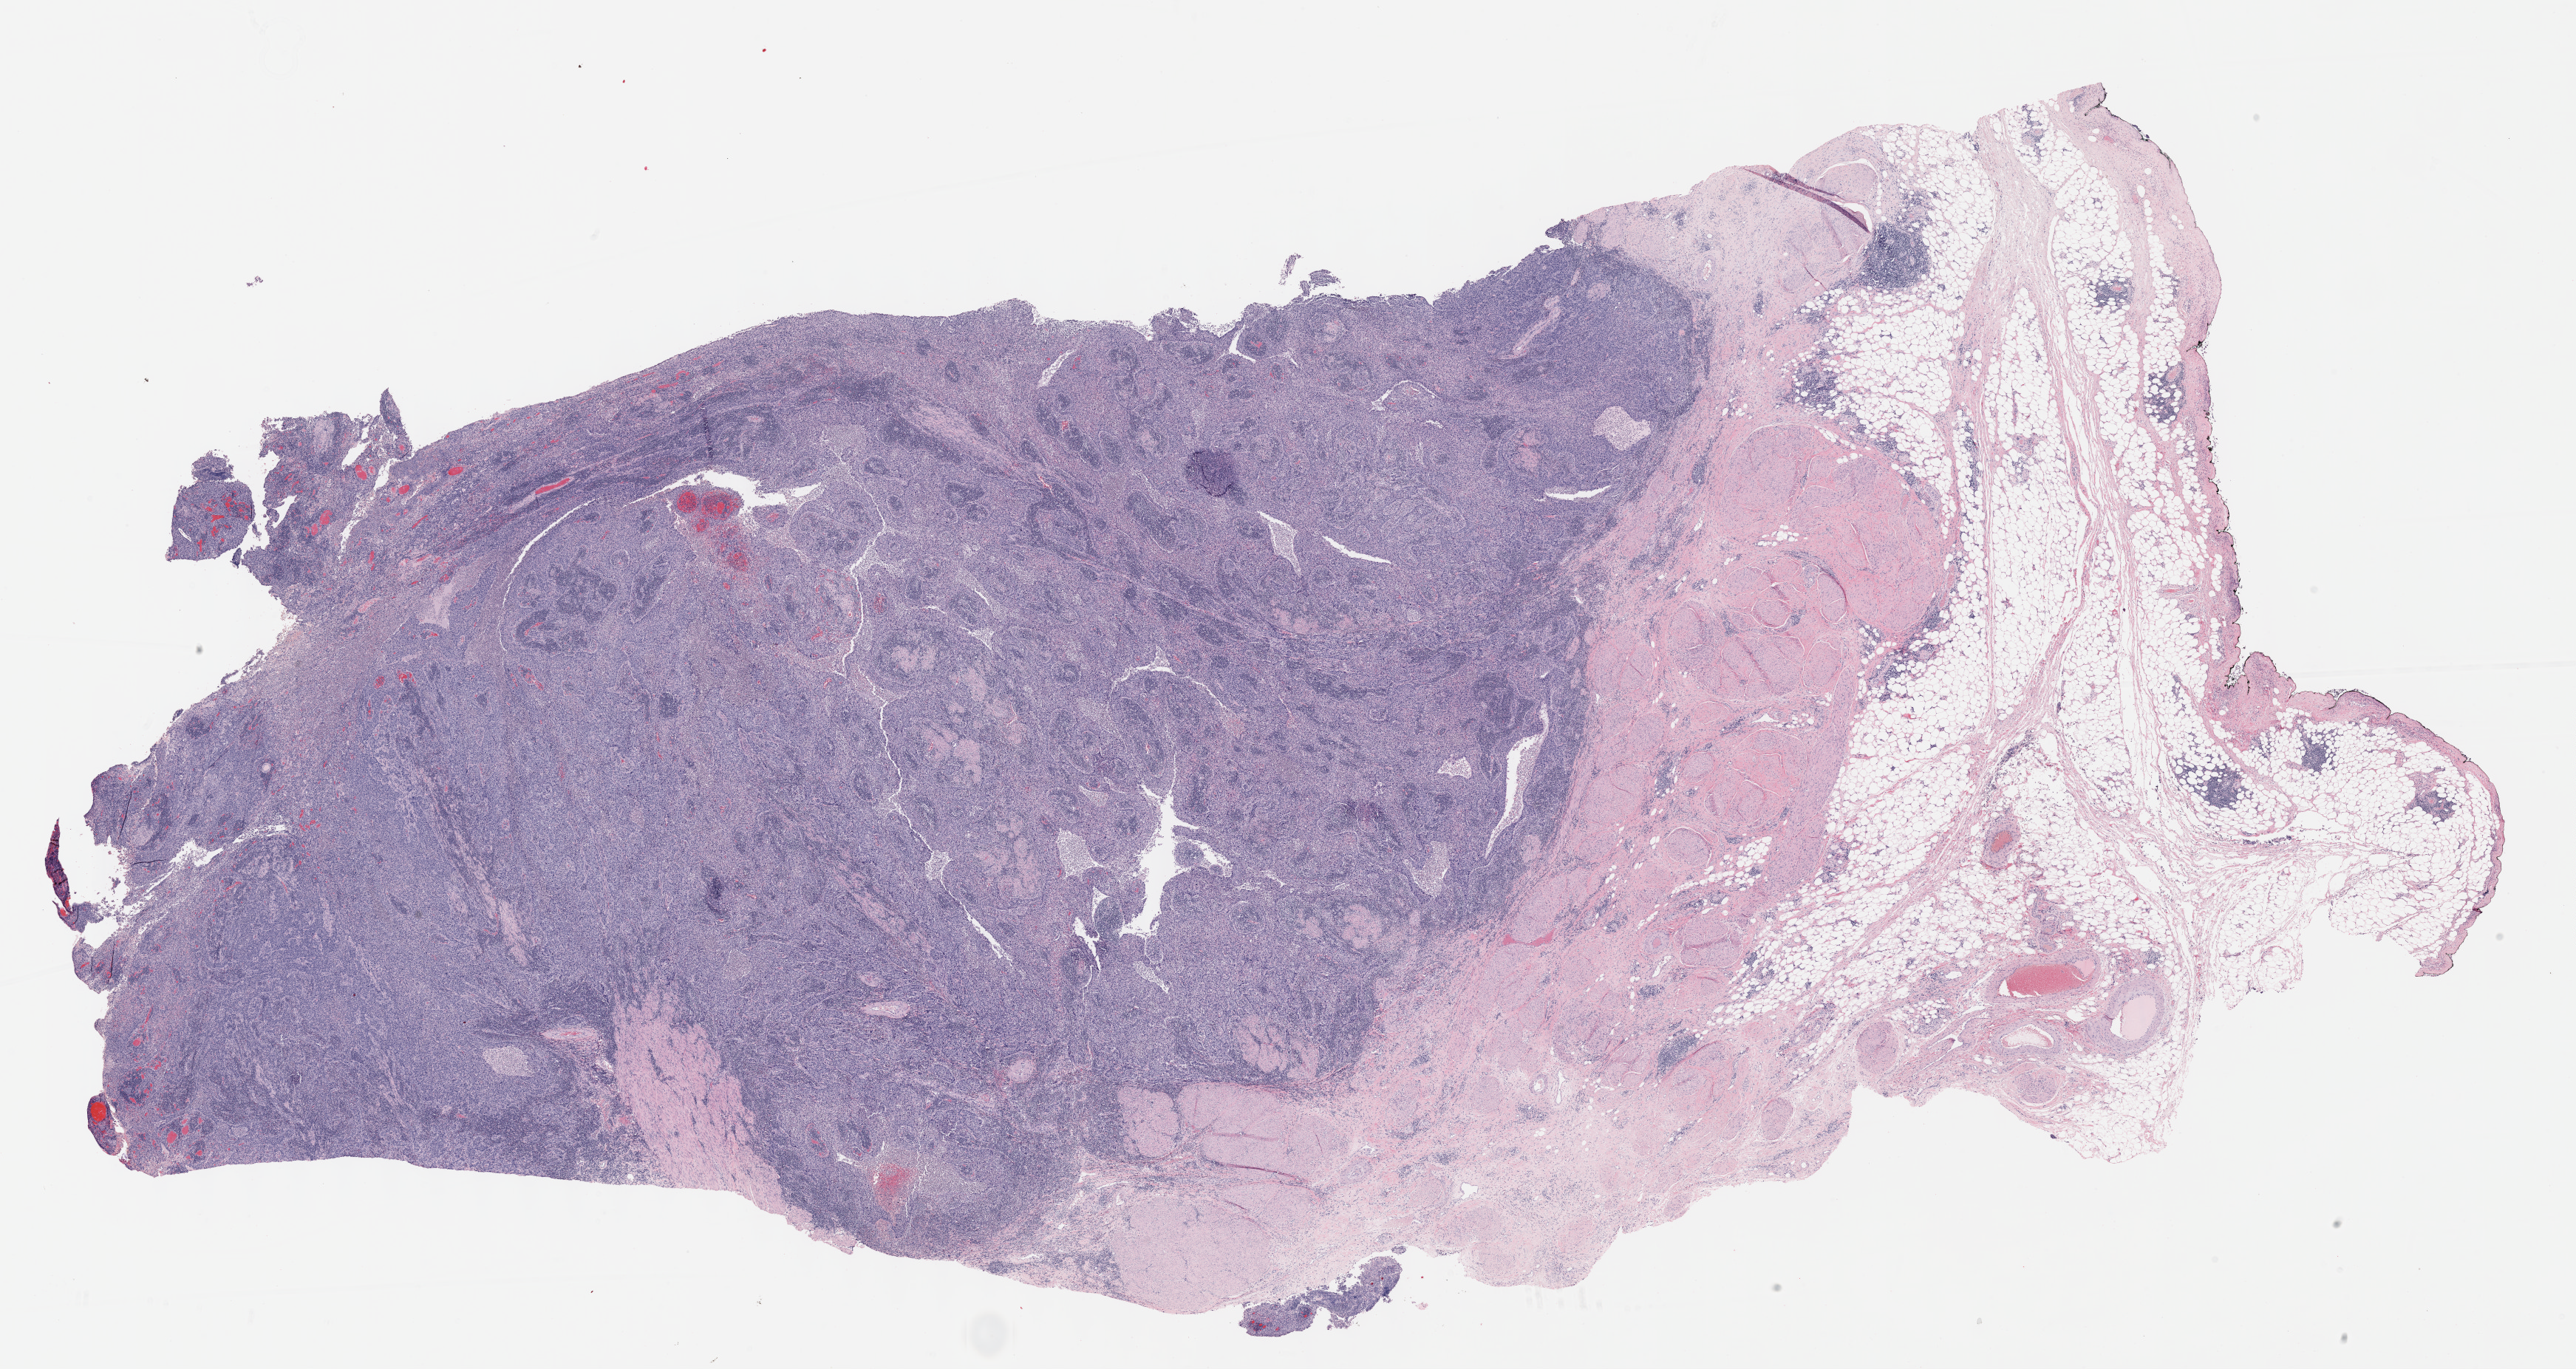
Digitized H&E tissue section (whole slide) — whole scanned area (about 28.2 x 15.0 mm, acquisition: 40x scan) shown as a low-resolution overview; formalin-fixed paraffin-embedded (FFPE) diagnostic section; bladder, primary tumour sample. Patient: male, age at initial diagnosis 78 years. Histologic grade: high grade.
* histologic diagnosis: Transitional cell carcinoma
* AJCC pathologic stage: IV